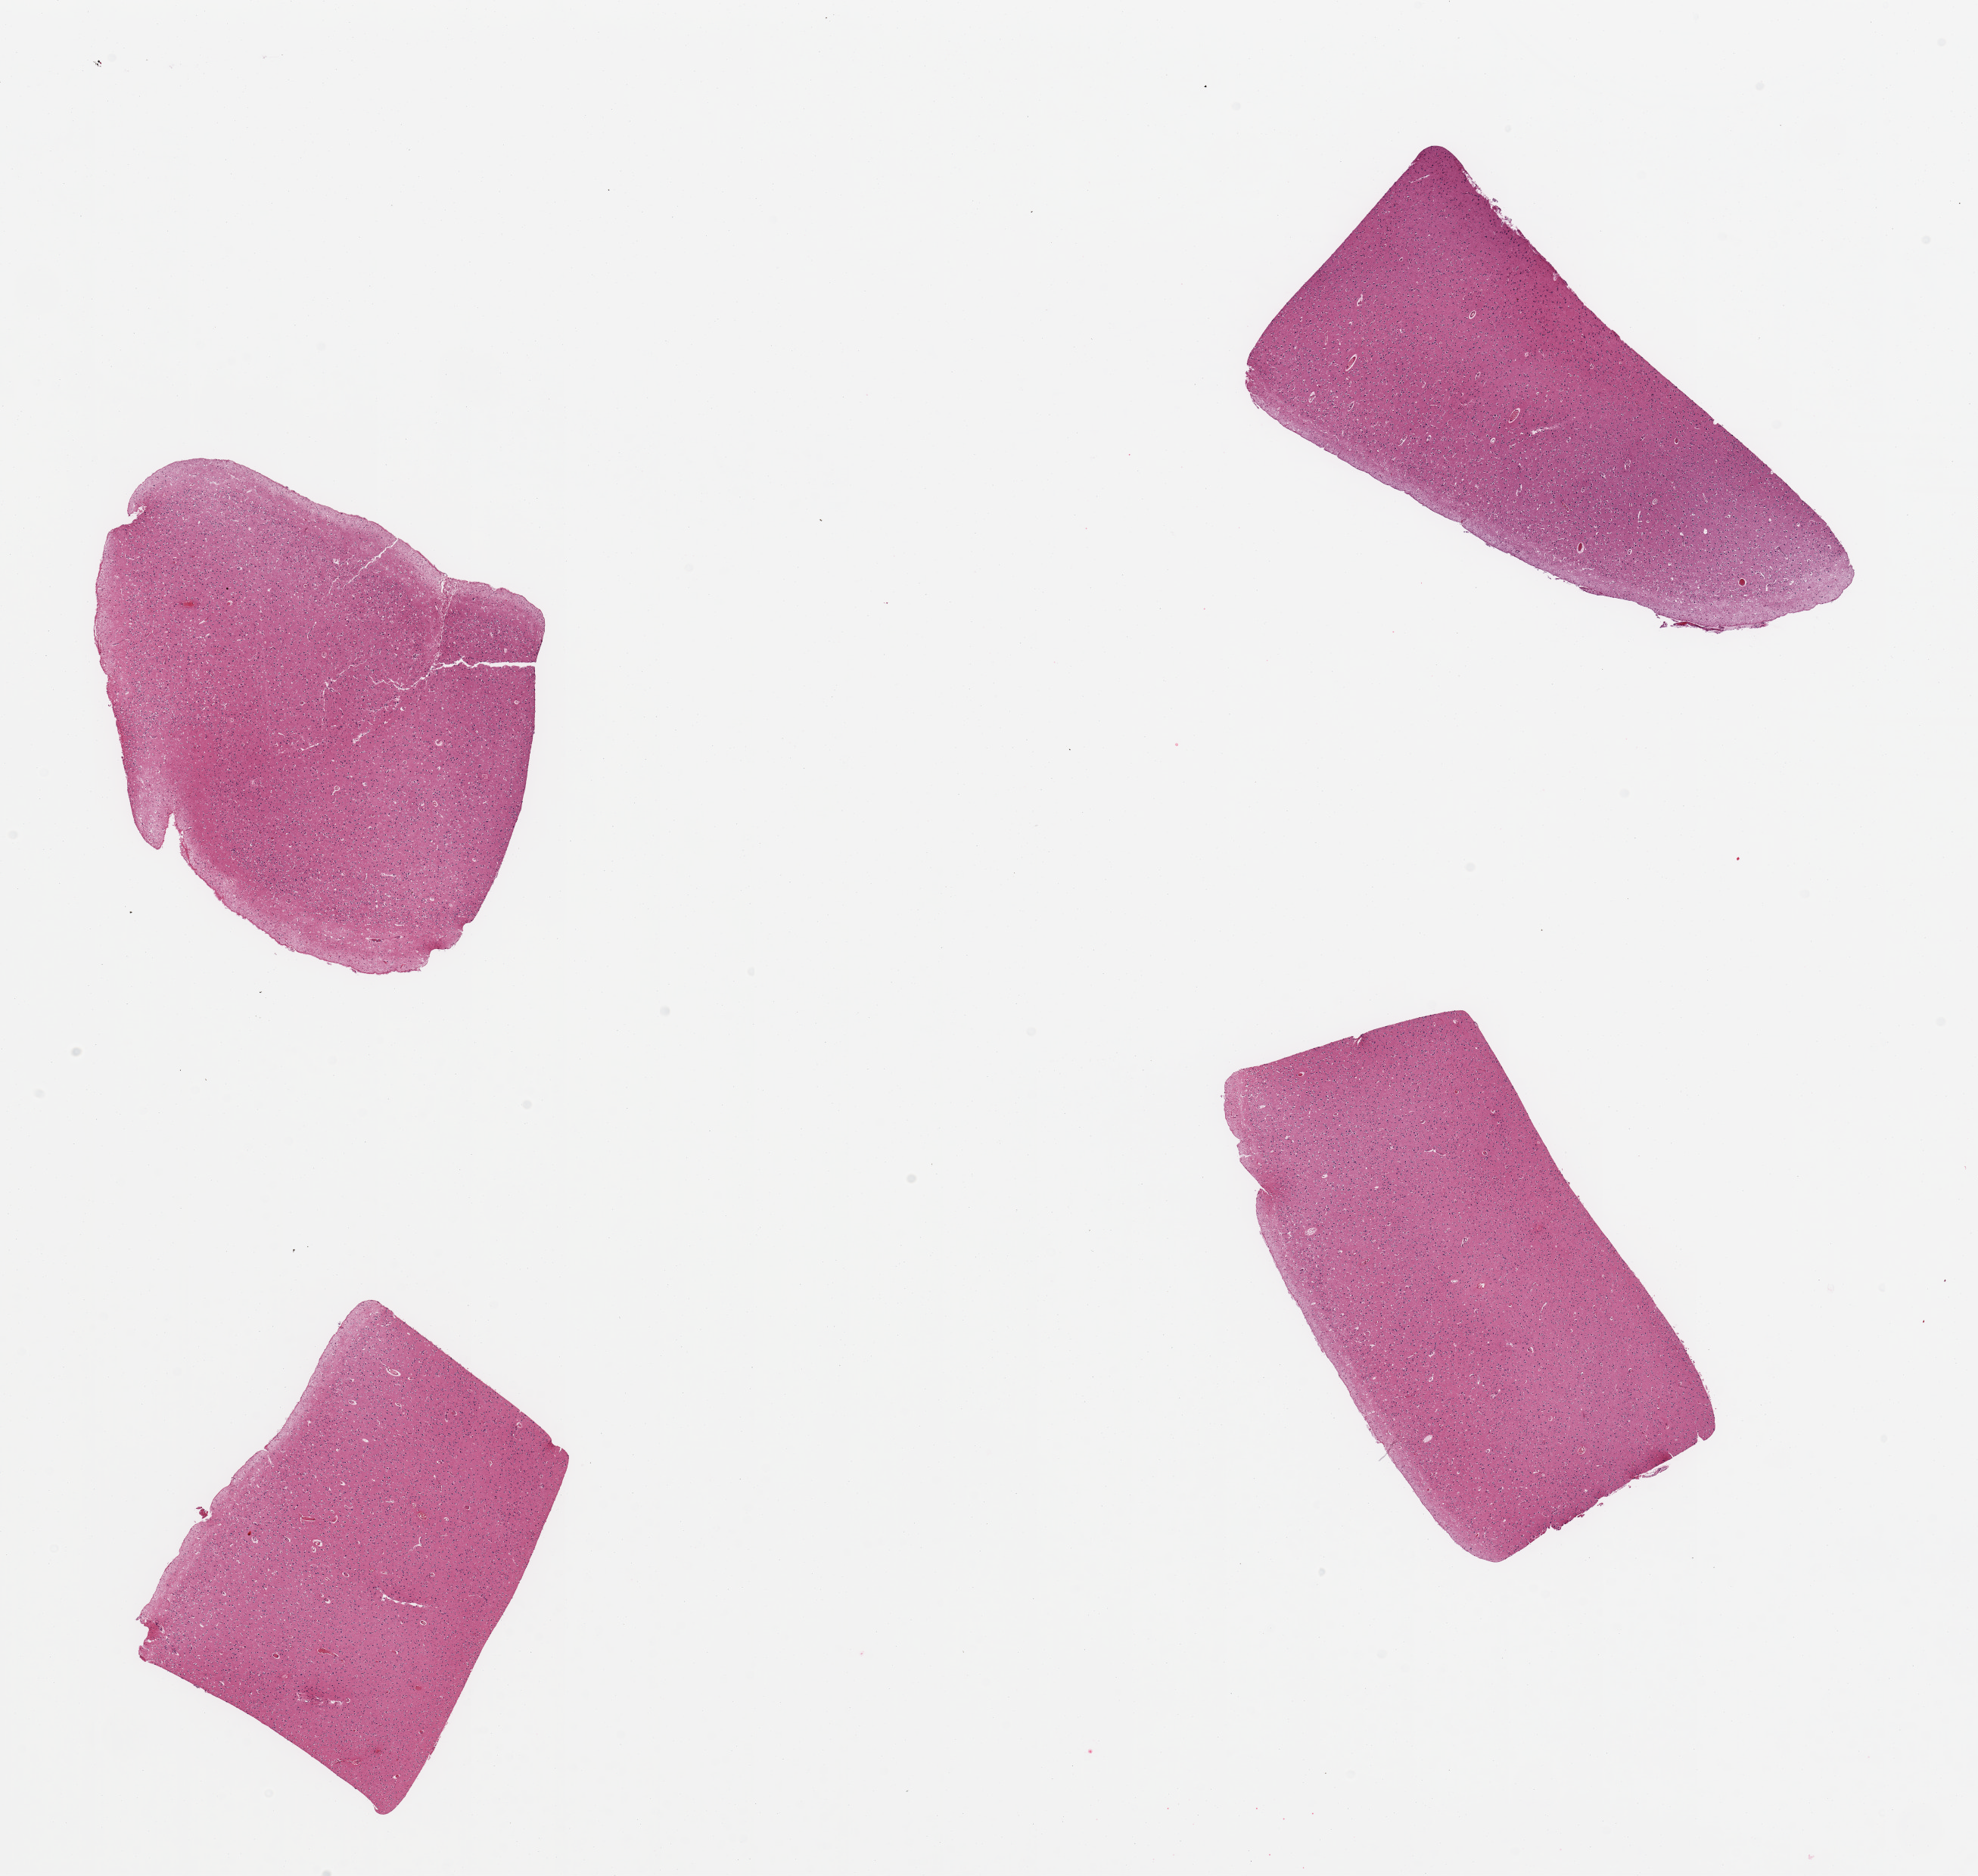
Whole-slide image, H&E stain, shown as a low-resolution overview of the whole scanned area (about 20.7 x 19.6 mm); PAXgene-fixed paraffin-embedded (PFPE) section; sampled site (target tissue): cerebral cortex; donor tissue sample. Female donor.
- review note (as recorded): 4 pieces